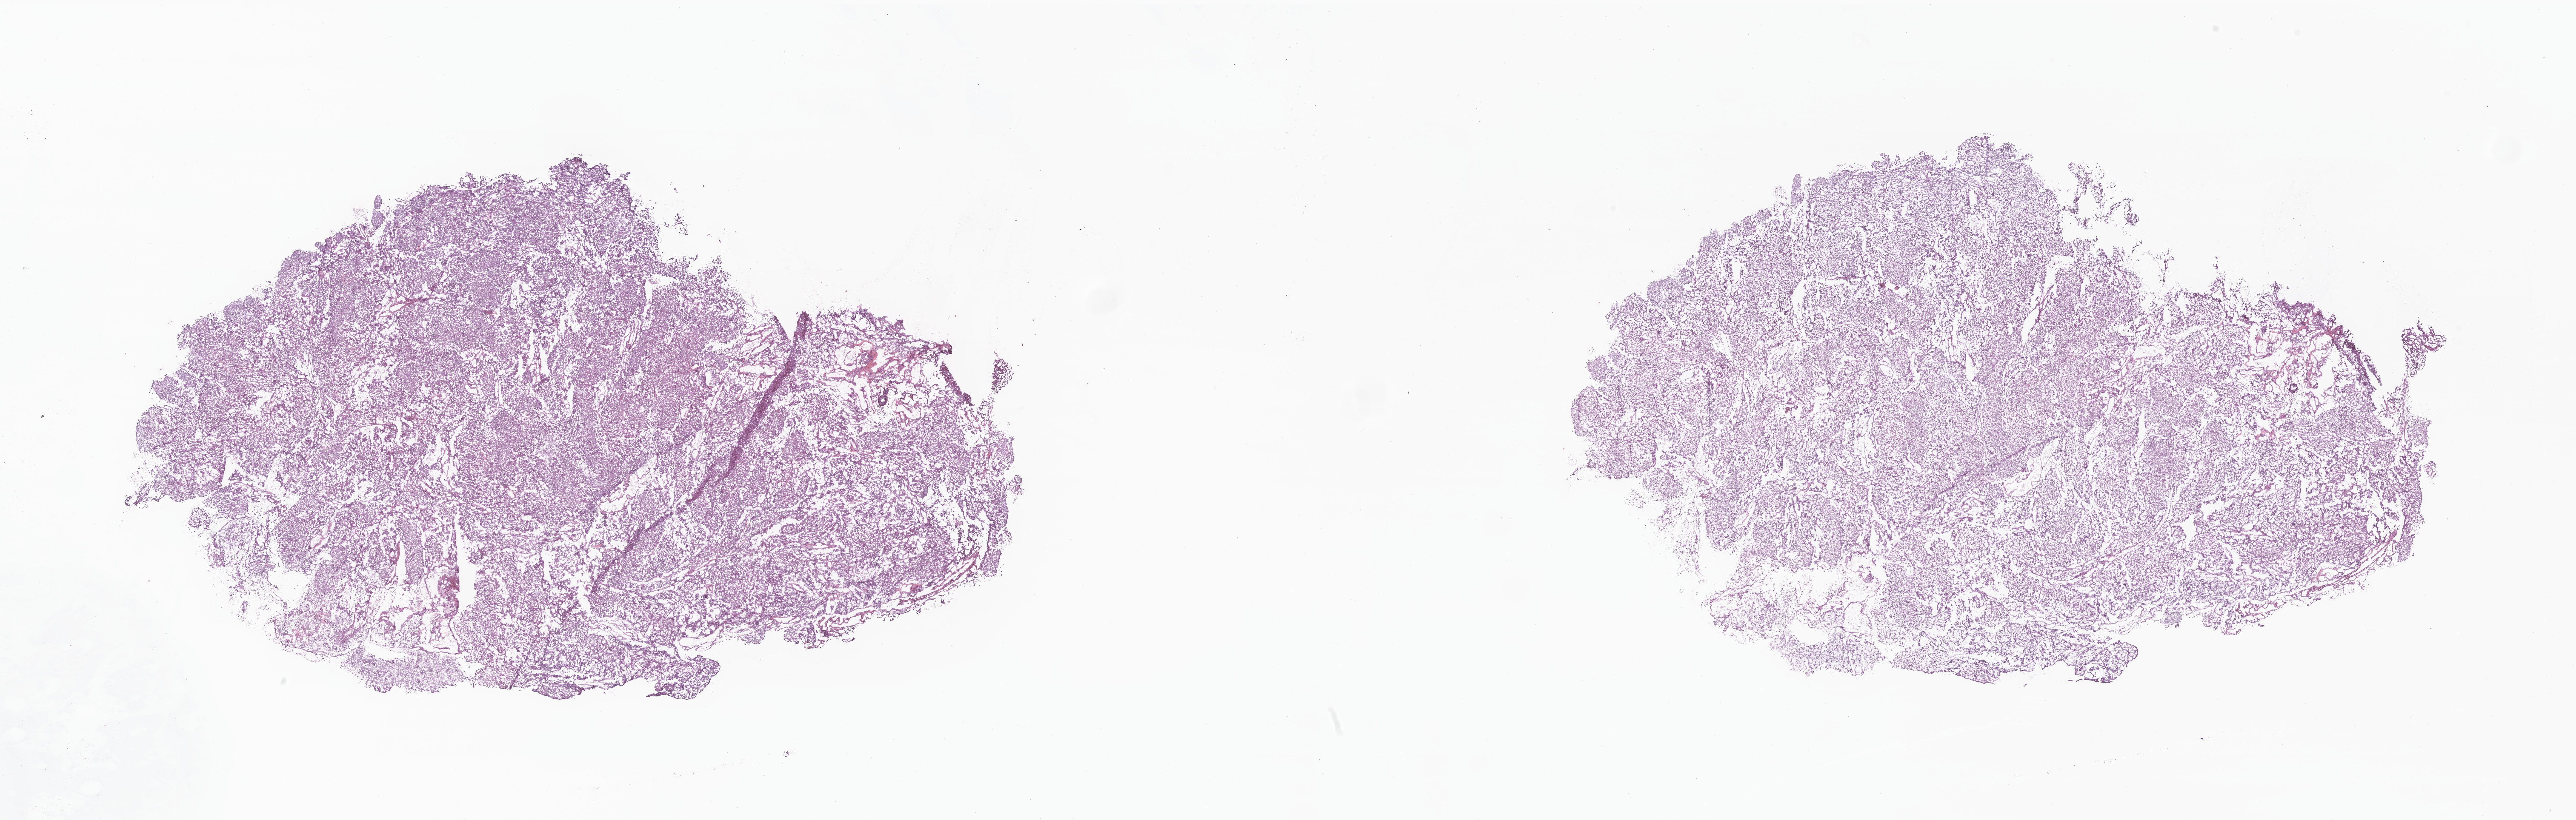
Whole-slide image, haematoxylin and eosin stain of tumor tissue from the frontal lobe, low-resolution overview of the scanned area, about 39.6 x 12.6 mm. Frozen section. Male patient, age 216 months (18 years).
Recorded diagnosis: Meningioma, NOS.